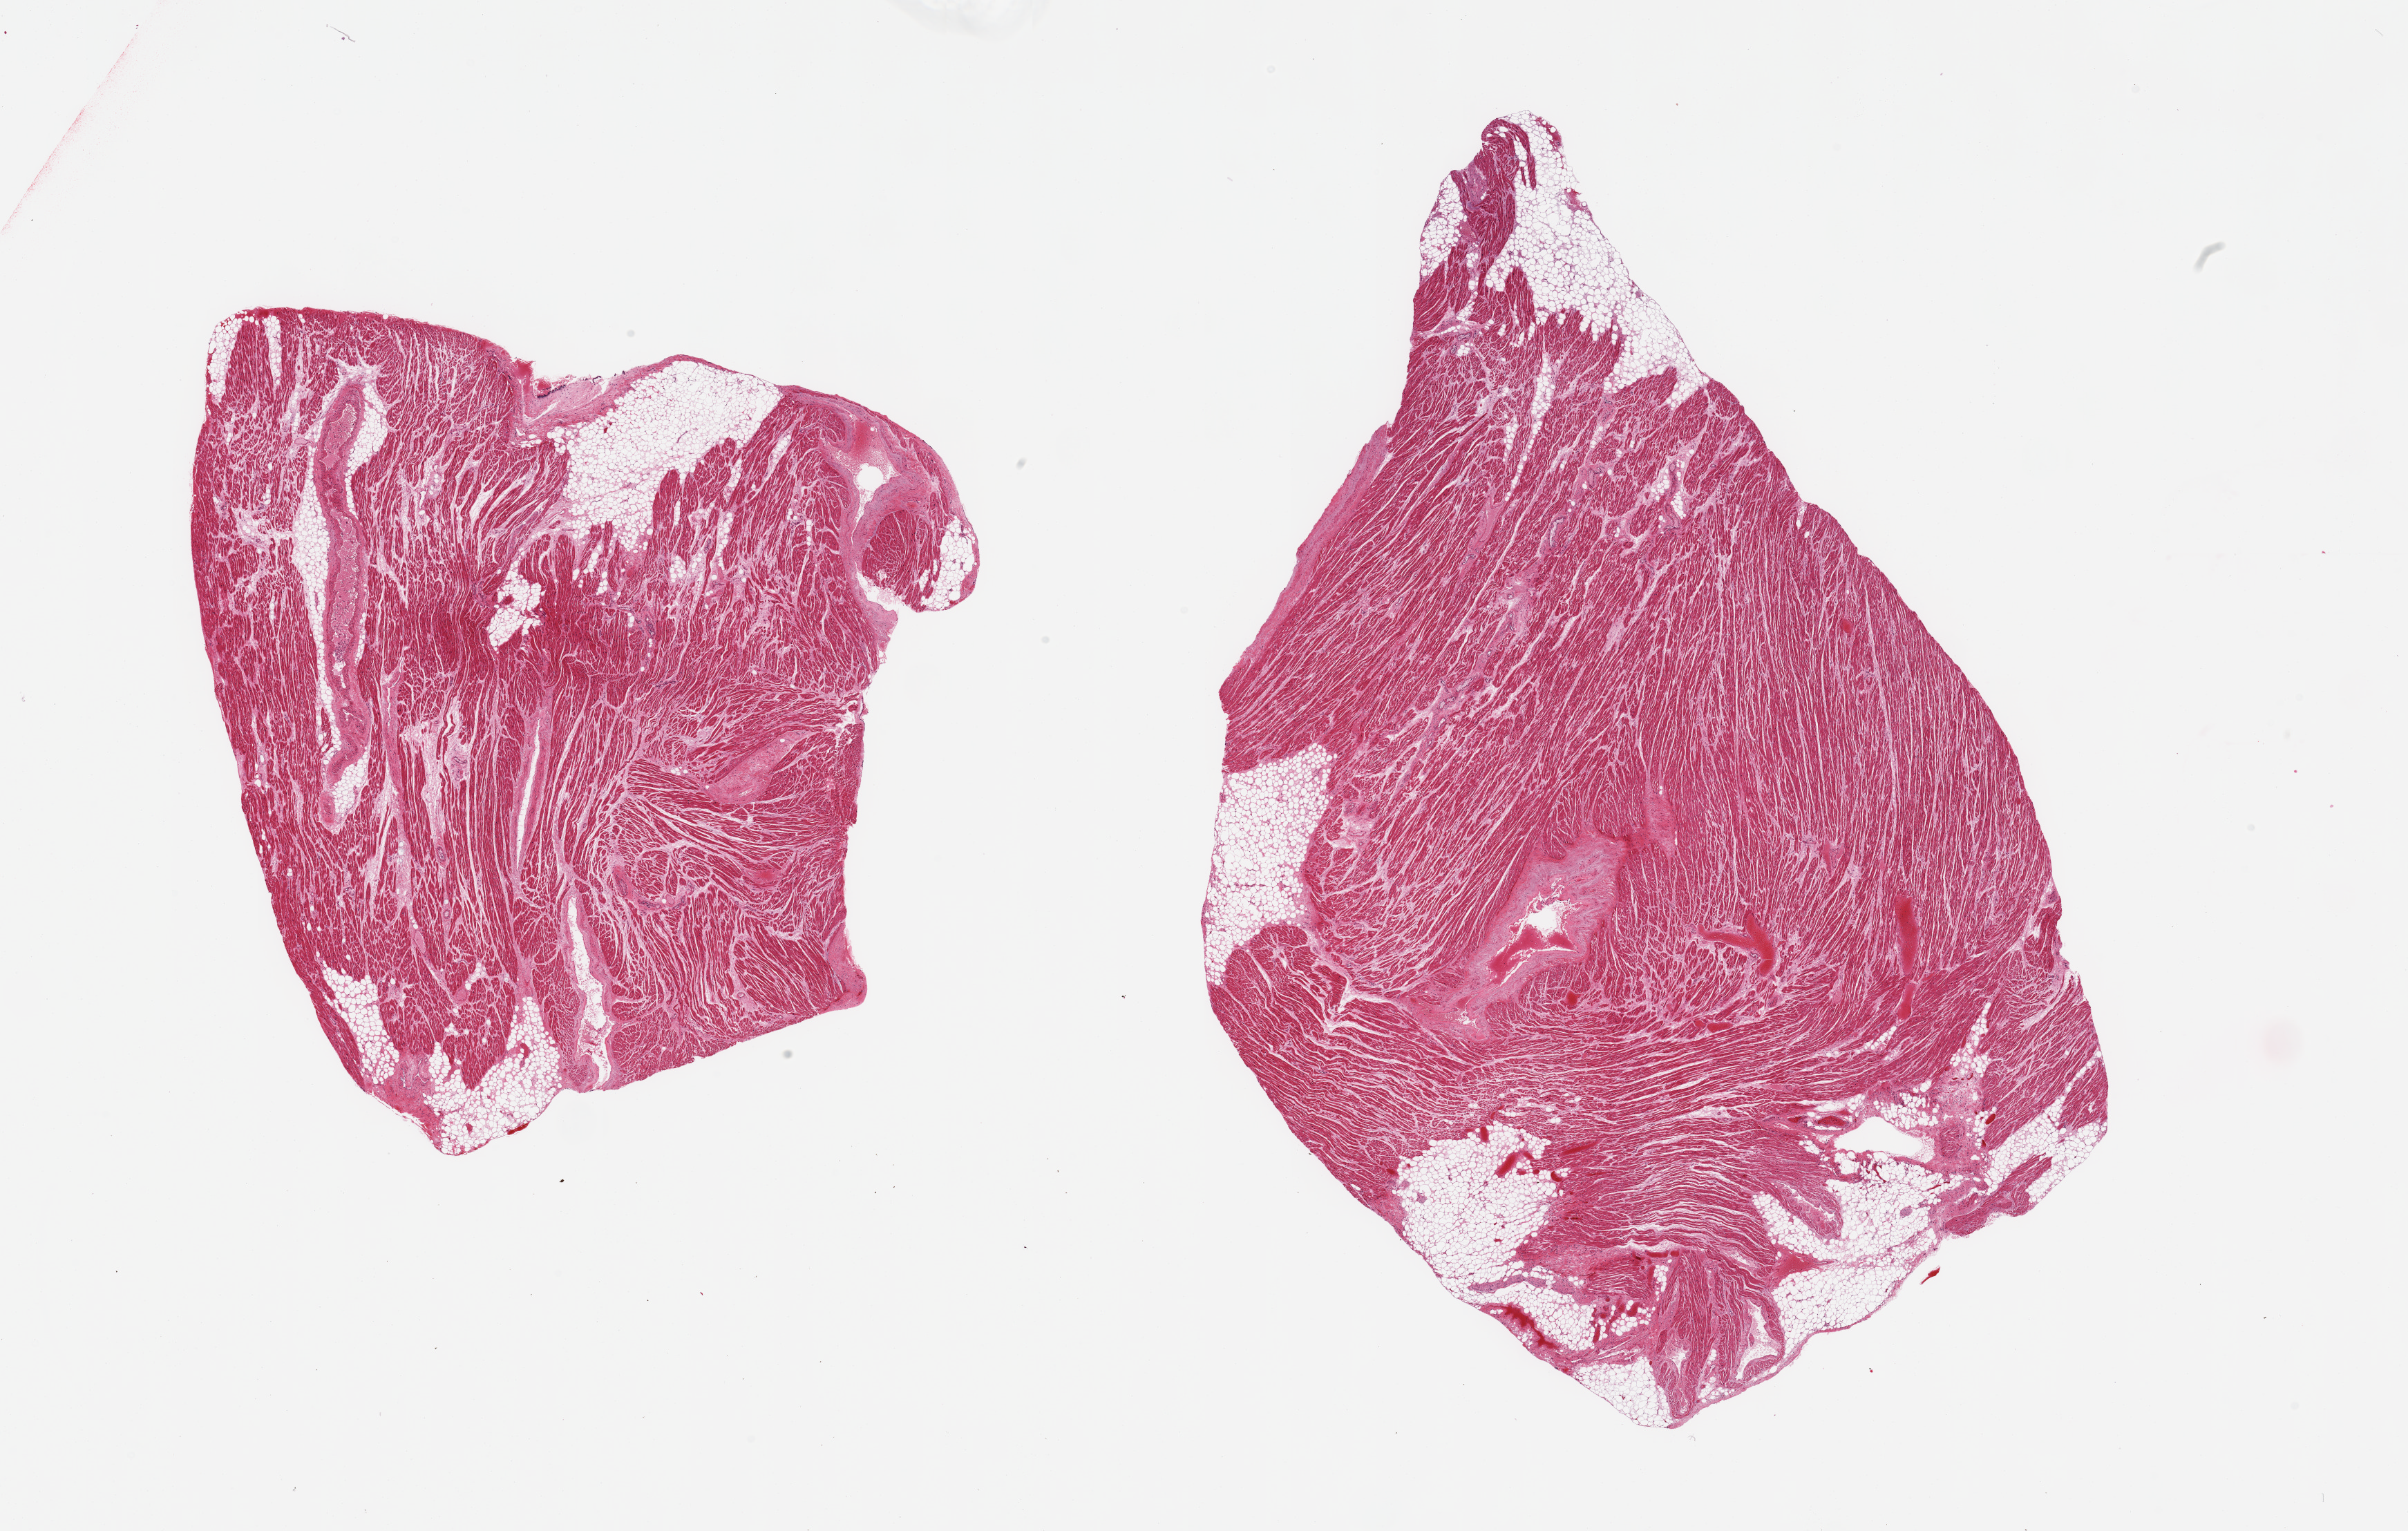
H&E whole-slide image — low-resolution overview of the scanned area, about 27.6 x 17.5 mm; PAXgene-fixed paraffin-embedded (PFPE) section; sampled site (target tissue): auricular appendage; donor tissue sample. Donor sex: male.
- reviewer comment on this tissue sample: 2 pieces, no abnormalities